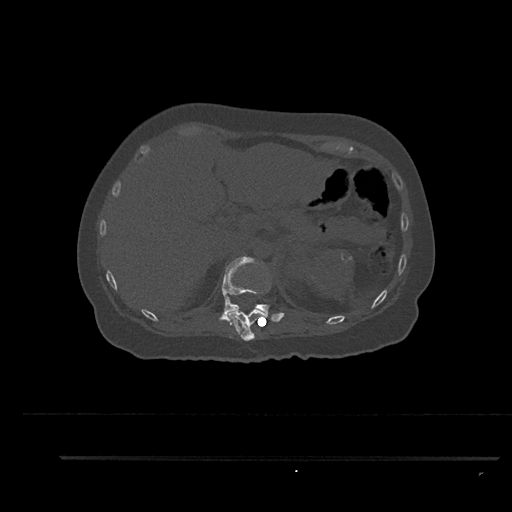
CT including the spine, one axial slice. Slice 289 of 797 in the series (ordered by position). Reconstruction kernel Br40s/3. 120 kVp. Bone window (W 1800 / L 400 HU). 0.5 mm slice thickness. 512 × 512 image matrix. Female patient, age 44 years. From the clinical record (not read from this slice): primary cancer: renal.
Structures marked on this image (semi-automatic segmentation, software-assisted and operator-edited):
- T11 vertebra: box from (x=229, y=307) to (x=266, y=341) px
- T12 vertebra: (x=219, y=256)–(x=285, y=322)